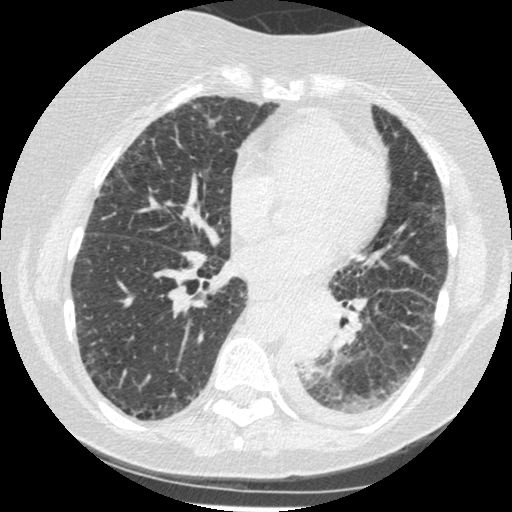
Low-dose screening chest CT, one axial slice. Position 99 of 341 along the scan axis. 120 kVp. Lung window (W 1500 / L -600 HU). 1.25 mm slice thickness. 512 × 512 image matrix, field of view 310 × 310 mm.
Structures marked on this image (outlined manually by an expert reader):
- lesion 1 (tumor, lower lobe of left lung): bounding box (x1, y1, x2, y2) in pixels: (287, 307, 335, 363)